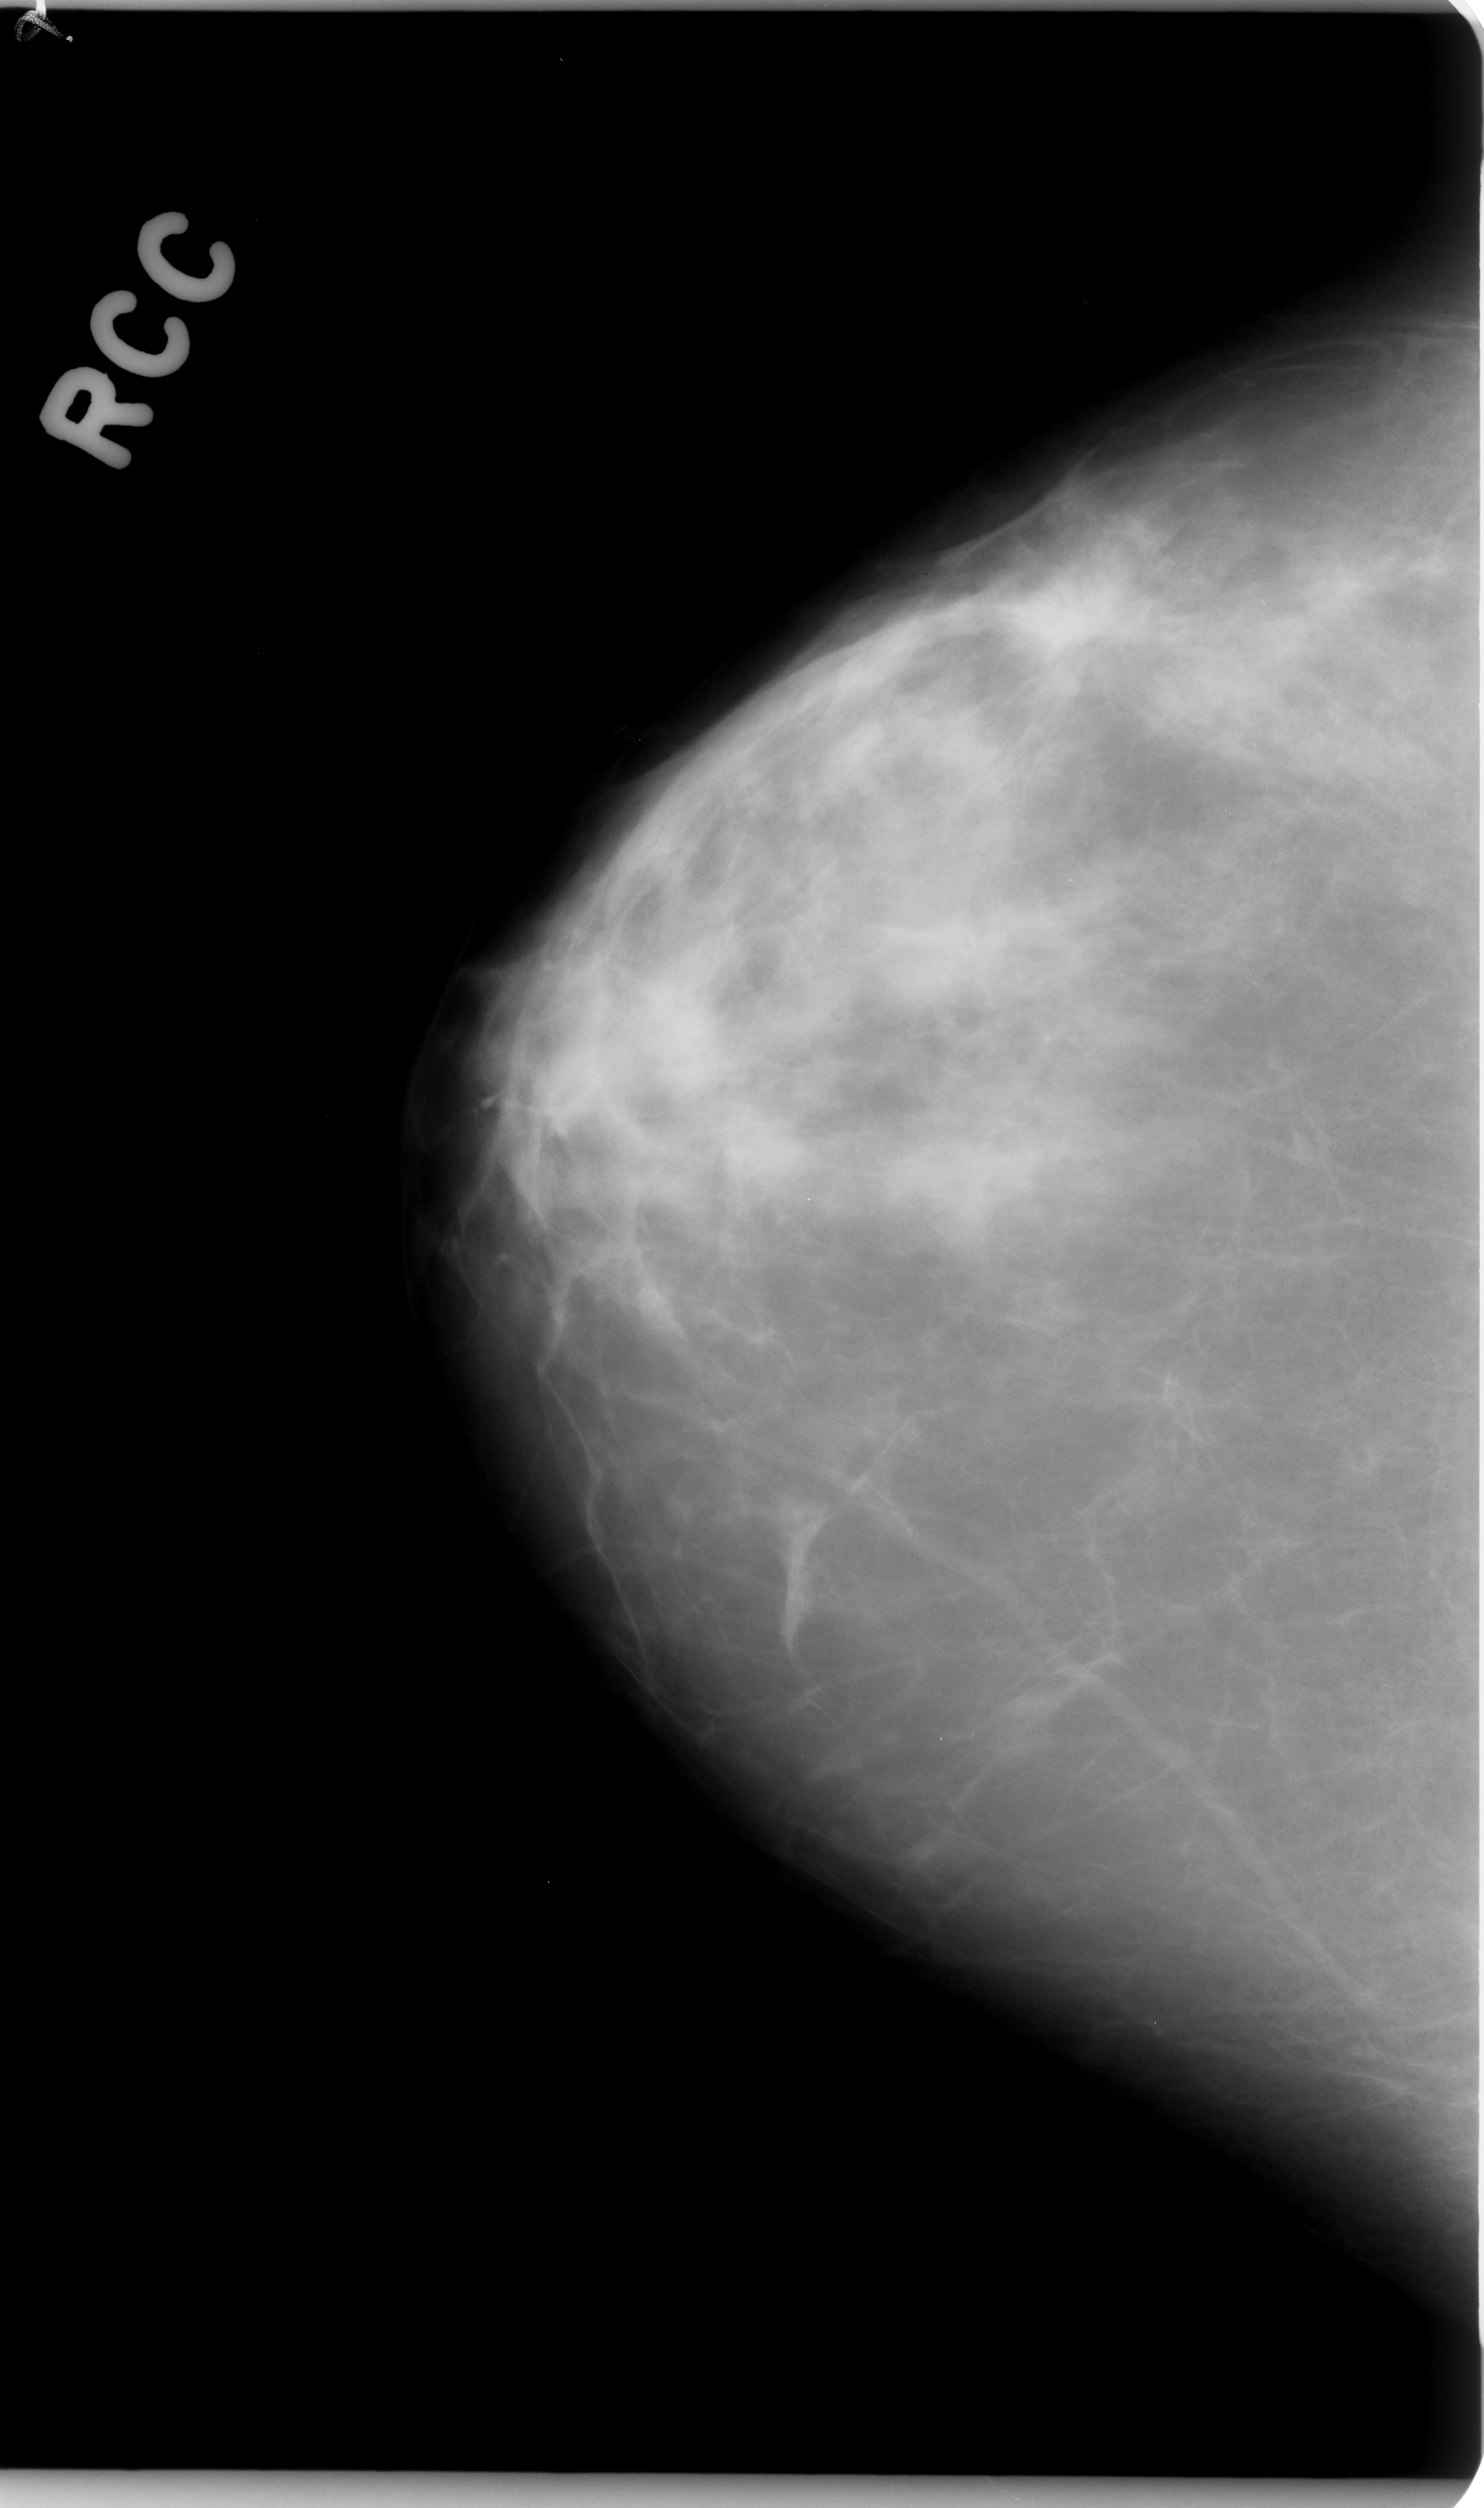
Digitized screen-film mammogram; right breast; CC view; breast composition: scattered fibroglandular densities (BI-RADS density category 2 of 4).
Radiologist-marked abnormalities on this image: mass, shape irregular, margins spiculated; BI-RADS assessment category 5; subtlety rating 5 on a 1 (subtle) to 5 (obvious) scale; pathology (as recorded): malignant.